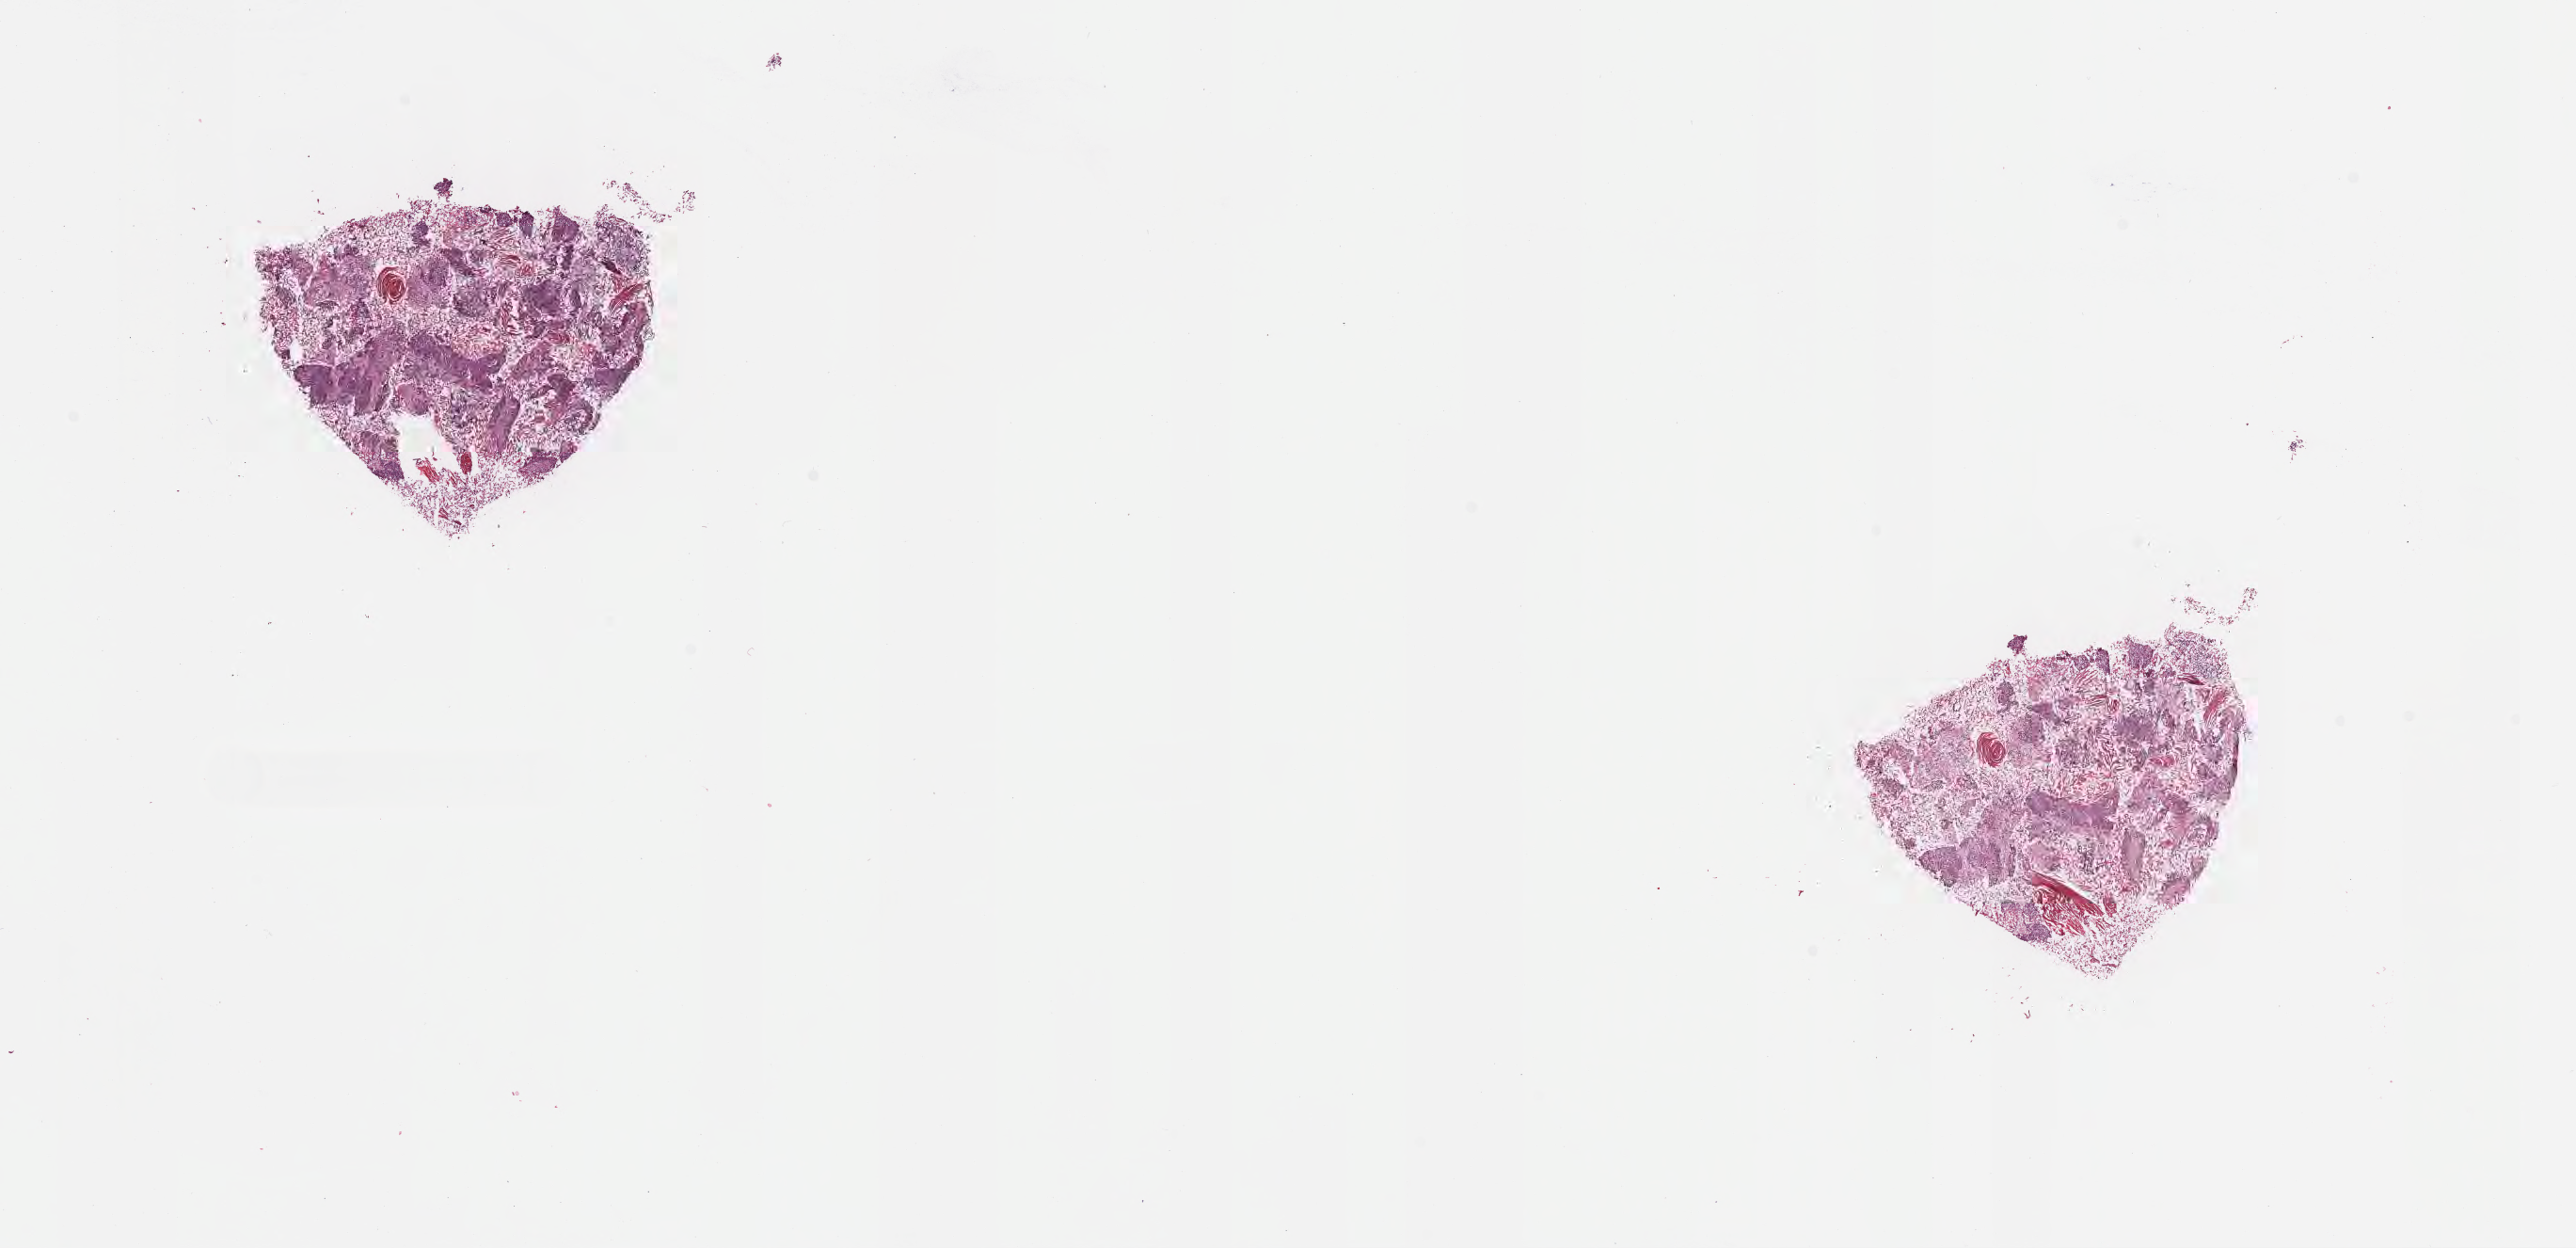
Whole-slide image, haematoxylin and eosin stain — a low-resolution overview of the entire scanned area, about 22.1 x 10.7 mm, cryosection, specimen: primary tumor, anatomic site: upper lobe of left lung. Male, age 59 years at initial diagnosis. Tumor grade: G1 (well differentiated). Slide review estimates, as recorded: tumor cells 80%, tumor nuclei 80%, stromal cells 20%, necrosis 0%, normal cells 0%. Infiltration values recorded for this section: lymphocyte infiltration 5%, monocyte infiltration 2%, neutrophil infiltration 7%.
• diagnosis: Squamous cell carcinoma, keratinizing, NOS
• AJCC pathologic stage: Stage IIIA